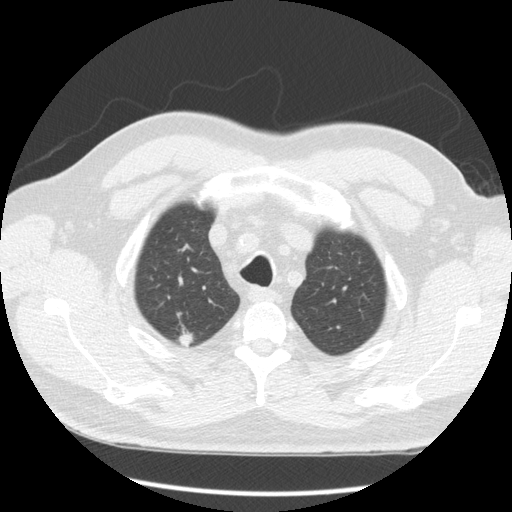
Axial slice from a low-dose chest CT screening exam. Baseline annual screen. Lung window (W 1500 / L -600 HU). 2.5 mm slice thickness. Standard (soft-tissue) reconstruction kernel (STANDARD). 120 kVp. Slice 20 of 163 in the series. Male, age 65 years at enrolment. Former smoker at enrolment.
Expert reader's lesion annotation, box from (x=162, y=321) to (x=205, y=358) px. The exam's reader record, not a measurement of the box and not confirmed to be the same lesion: non-calcified nodule or mass ≥4 mm, right upper lobe, 10 × 9 mm, spiculated (stellate) margins, soft tissue attenuation. Later outcome: lung cancer diagnosed 103 days after this screen — squamous cell carcinoma, NOS, right upper lobe, poorly differentiated (G3), stage IA (AJCC 6th edition), 5 mm at pathology.